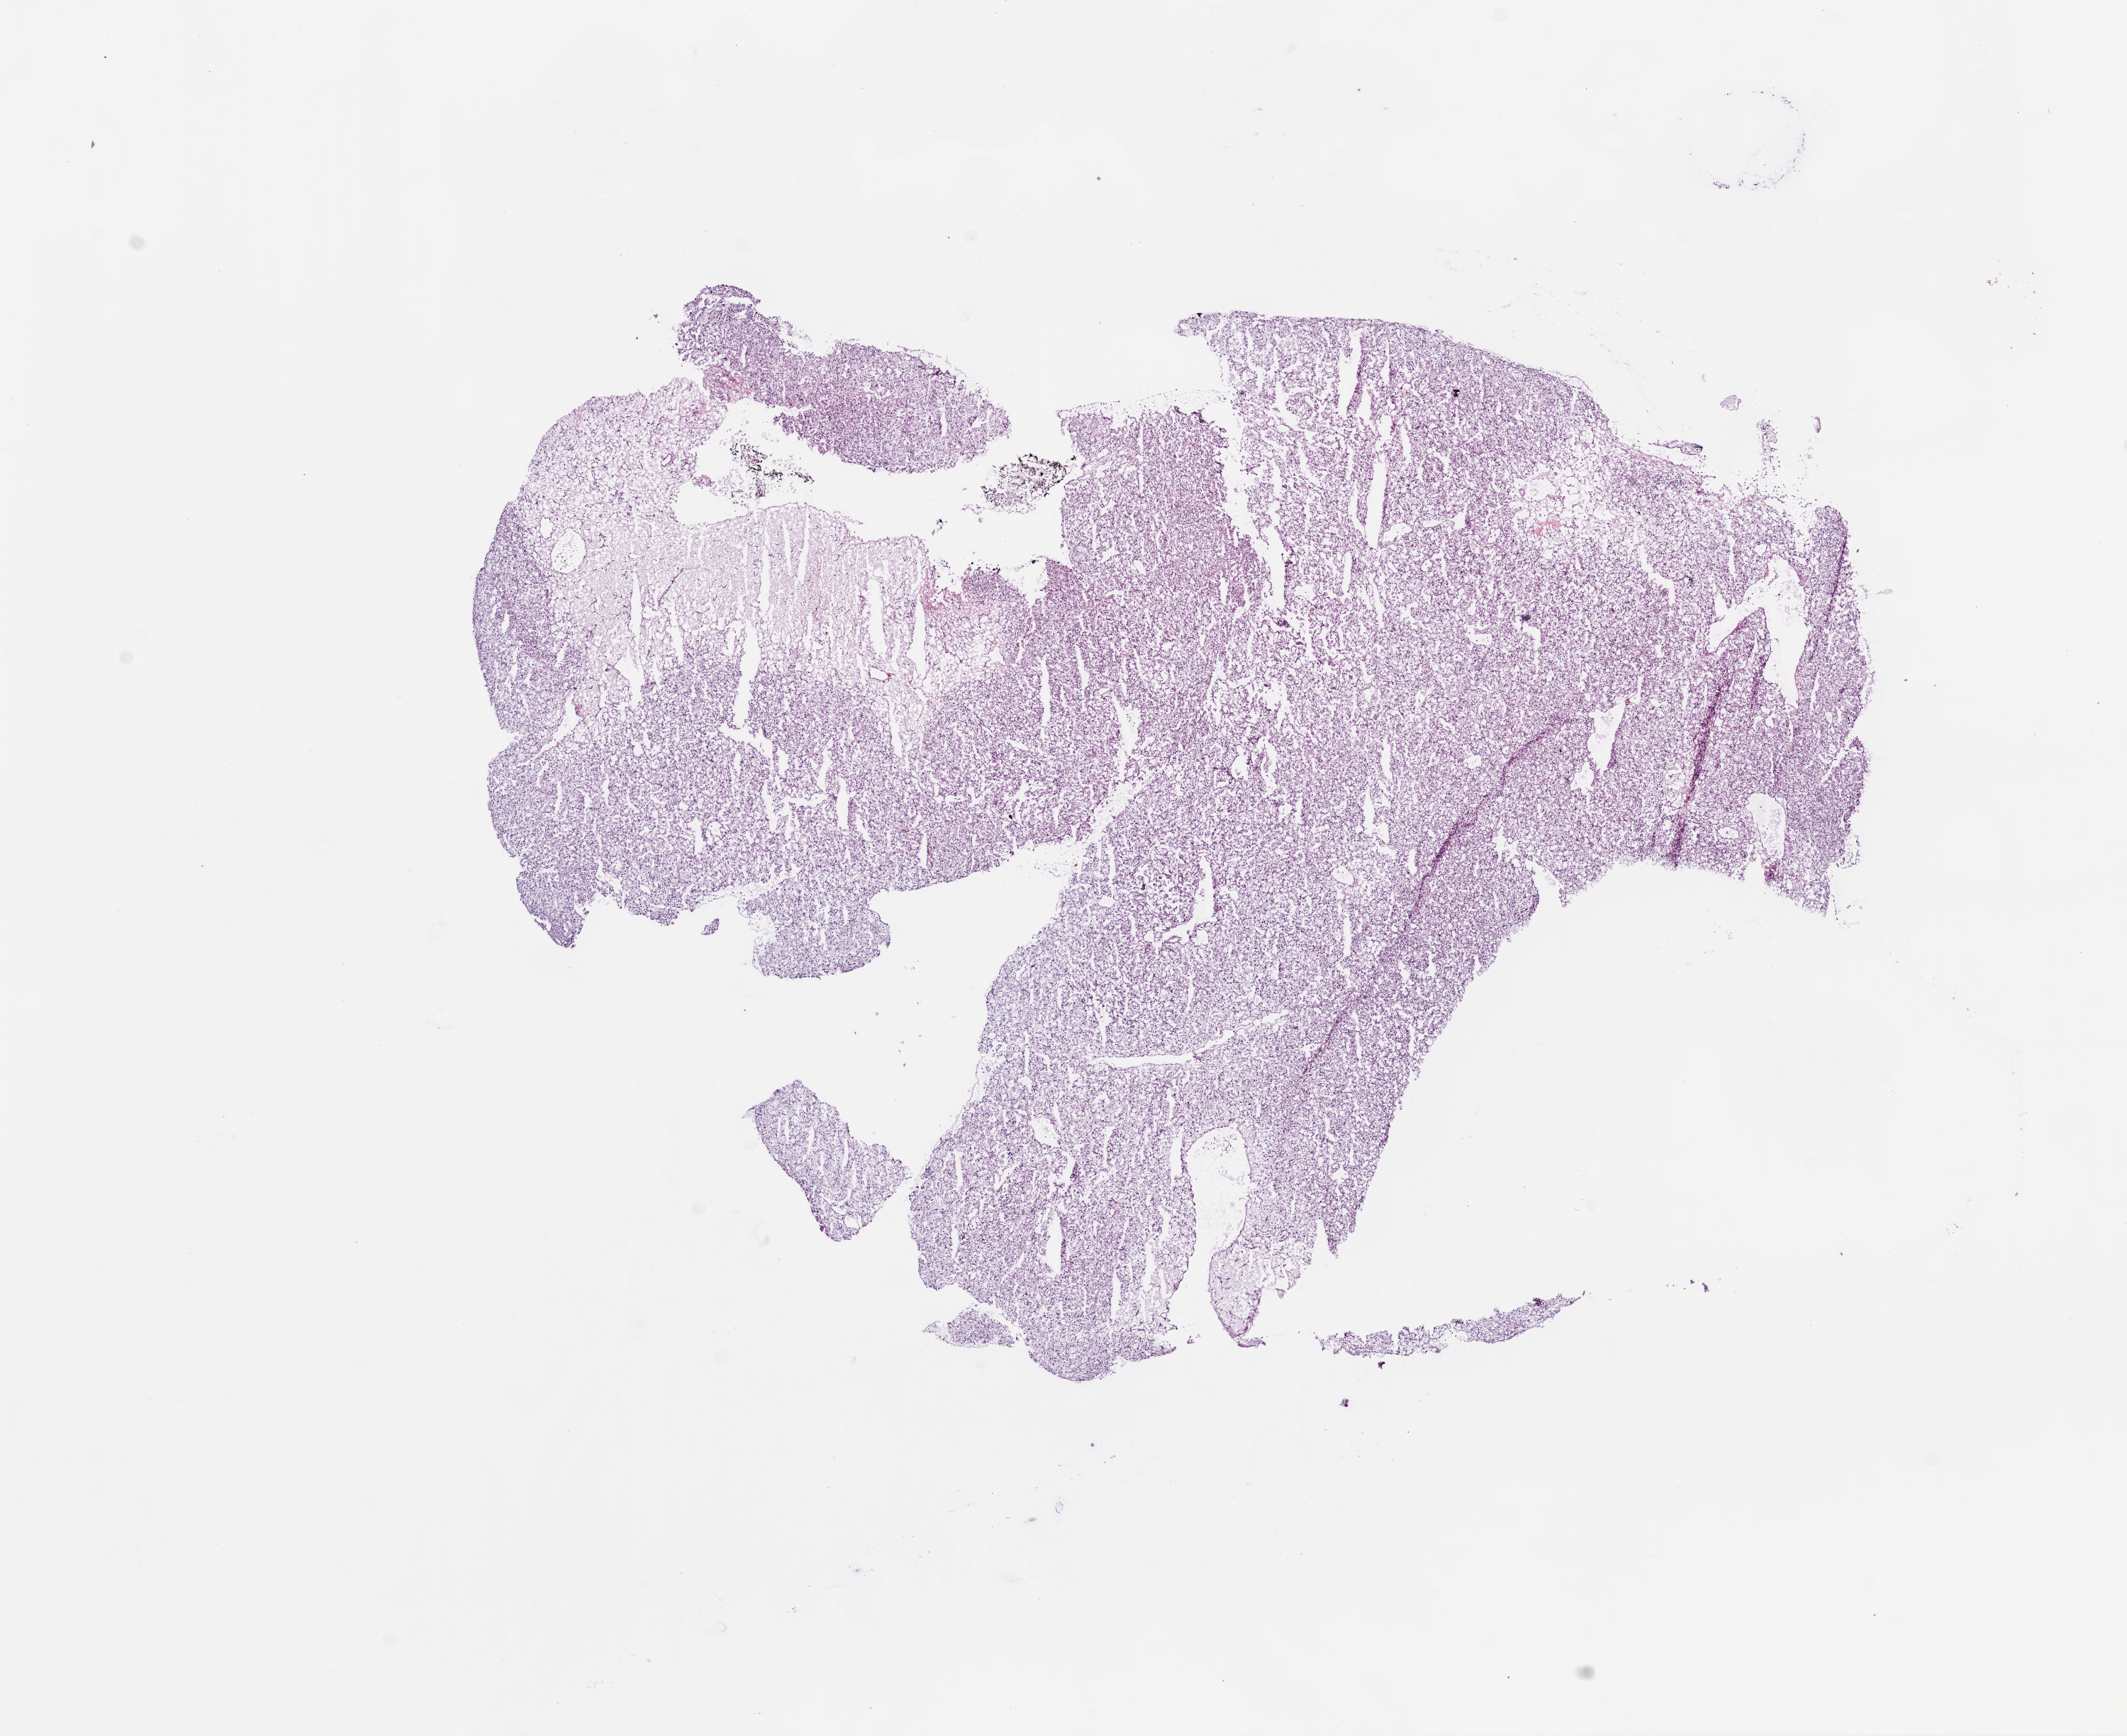
H&E whole-slide image — a low-resolution overview of the entire scanned area, about 12.0 x 9.8 mm; frozen section from the bottom of the tissue portion; sample: primary tumour, kidney. Male patient; age at initial diagnosis 61 years. Histologic grade: G2 (moderately differentiated). Pathologist review of this section (percent, as recorded): tumour cells 90%, tumour nuclei 85%, normal cells 0%, stromal cells 10%, necrosis 0%.
* lymph nodes positive (case pathology): 0 of 2 examined
* pathologic diagnosis: Clear cell adenocarcinoma, NOS
* AJCC pathologic stage: I